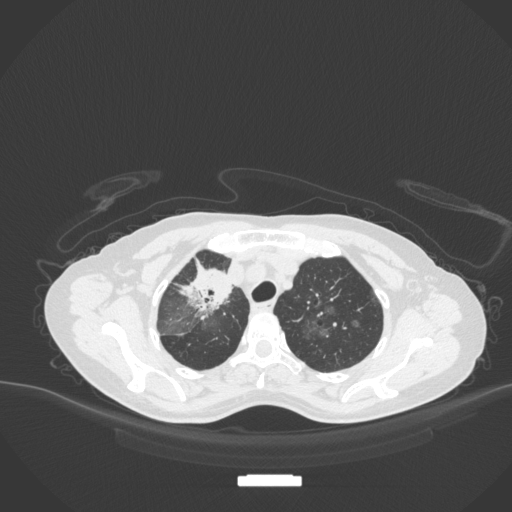
Chest CT, one axial slice. Position 263 of 311 along the scan axis. Reconstruction kernel B31f. Lung window (W 1500 / L -600 HU). 512 × 512 image matrix. Female patient, age 59 years. Case-level facts recorded for this patient, not image findings: clinical TNM (as recorded): T3 N0 M0.
Outlined on this slice (rectangle marked by the reading radiologist):
- lung tumour (recorded histology: adenocarcinoma): bounding box [x1, y1, x2, y2] px = [174, 260, 238, 319]